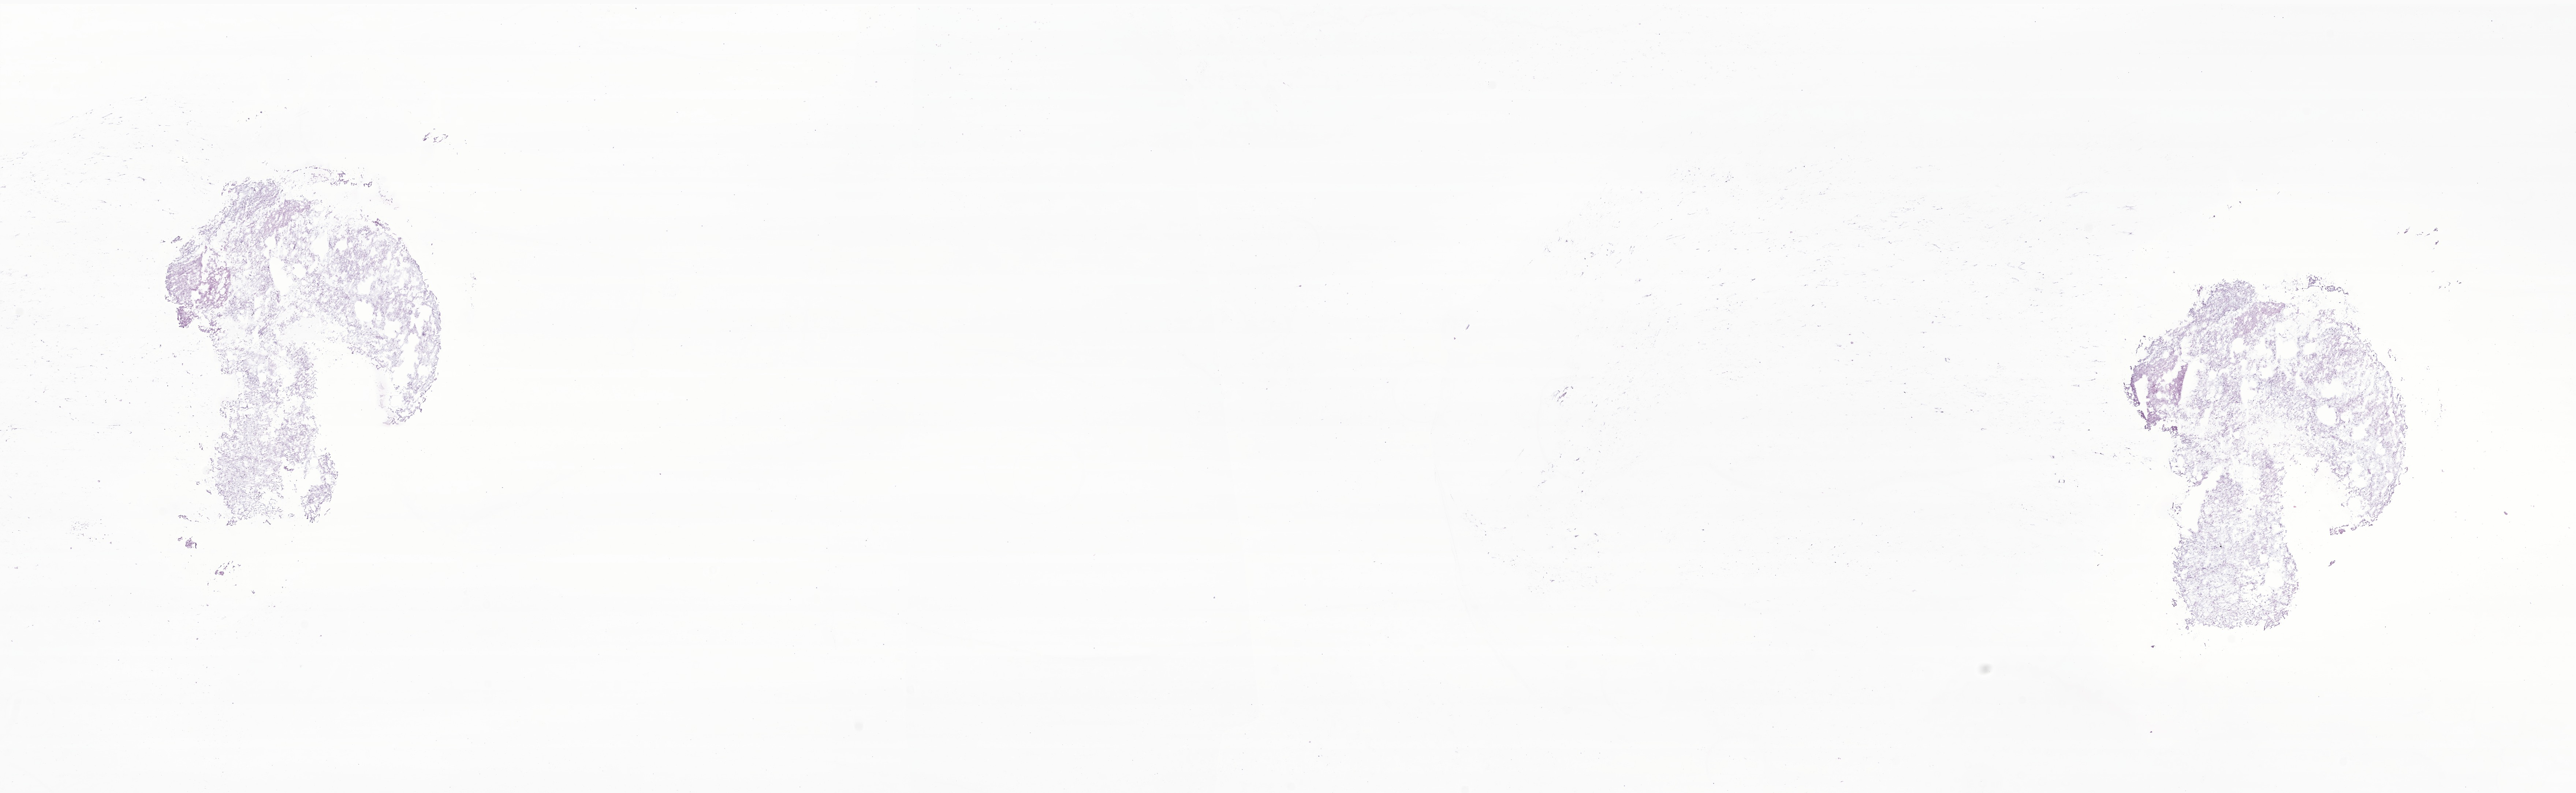
Hematoxylin and eosin (H&E) whole-slide image of tumor tissue from the brain — low-resolution overview of the scanned area, about 29.7 x 9.1 mm, frozen section. Patient female; age 52 months (4 years 4 months).
Diagnosis: Dysembryoplastic neuroepithelial tumor.